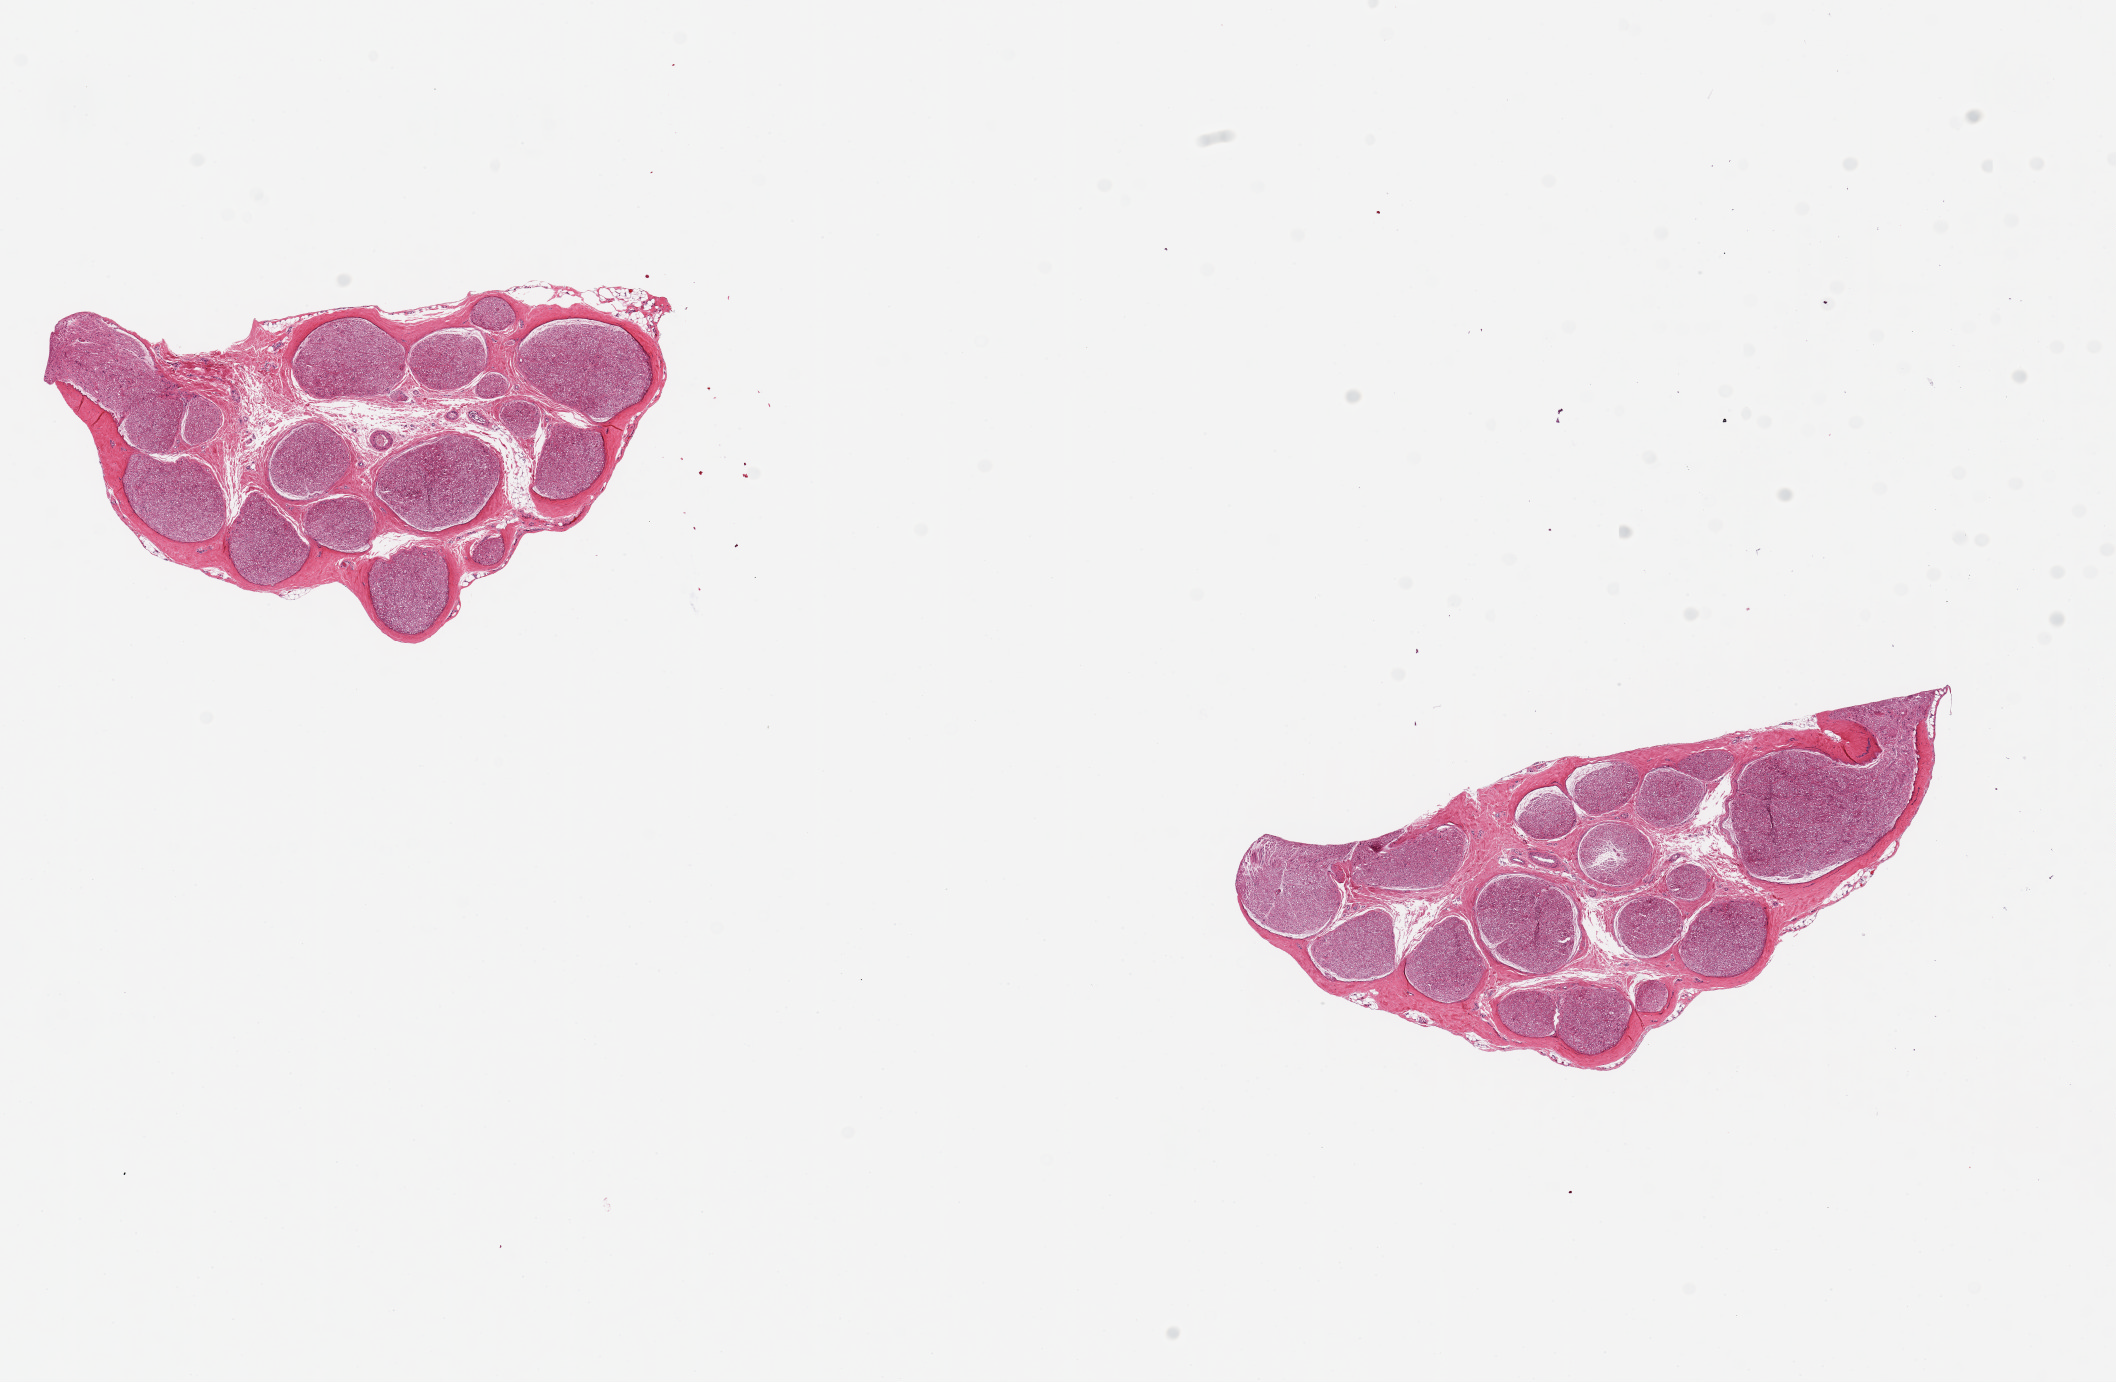
Digitized H&E-stained section, low-resolution overview of the scanned area, about 16.7 x 10.9 mm (acquisition: 20x scan); PAXgene-fixed paraffin-embedded (PFPE) section; target tissue: tibial nerve; donor tissue sample. Donor sex: male.
* reviewer comment on this tissue sample: 2 pieces ~3.5mm d. Good clean specimens